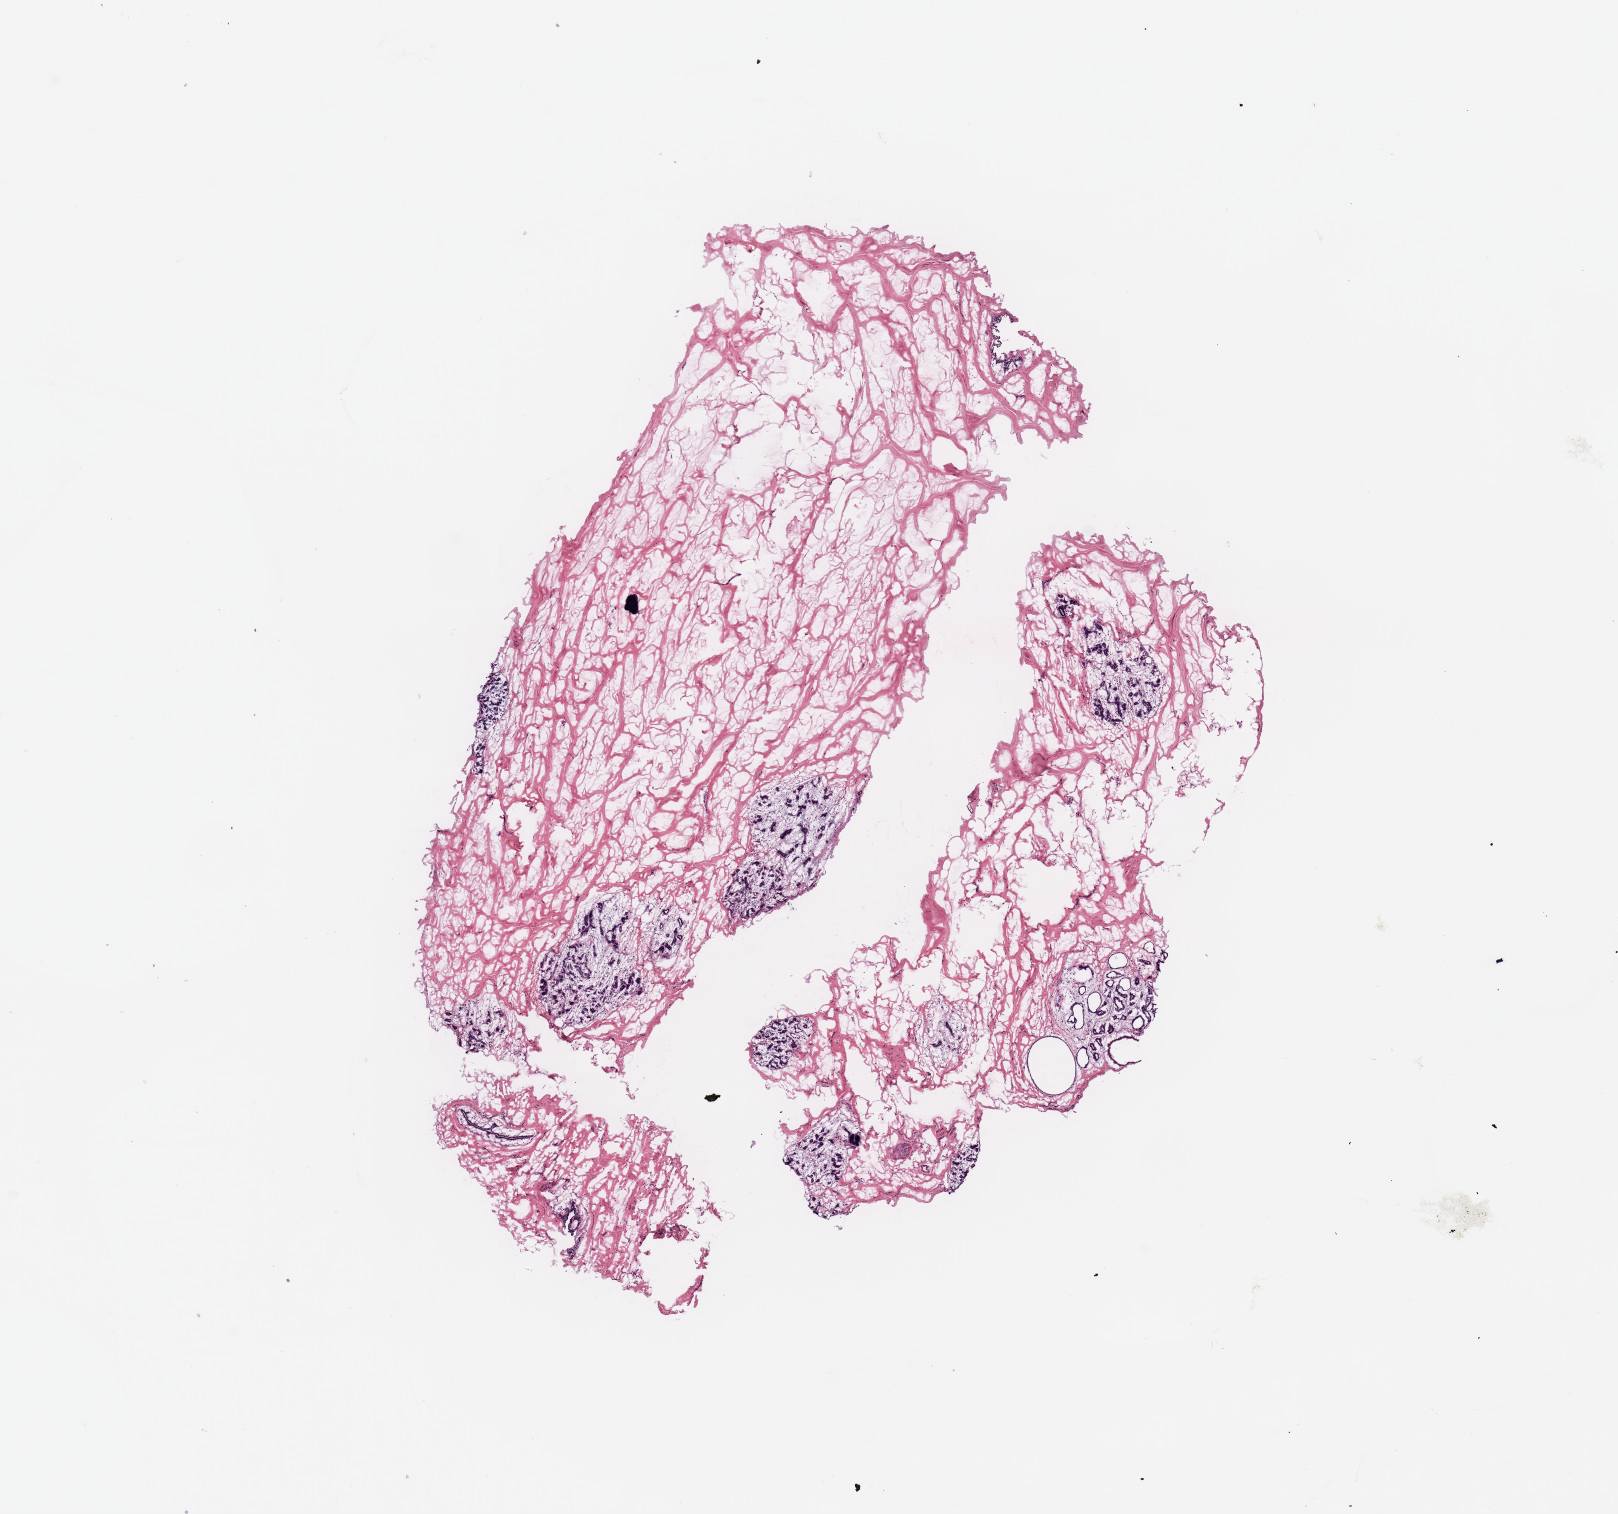
Whole-slide histology image, Hematoxylin and eosin (H&E) stained — a low-resolution overview of the entire scanned area, about 12.8 x 12.0 mm (slide scanned at 20x); breast, tissue type not recorded.
Patient diagnosis (cohort enrolment): breast cancer (breast).